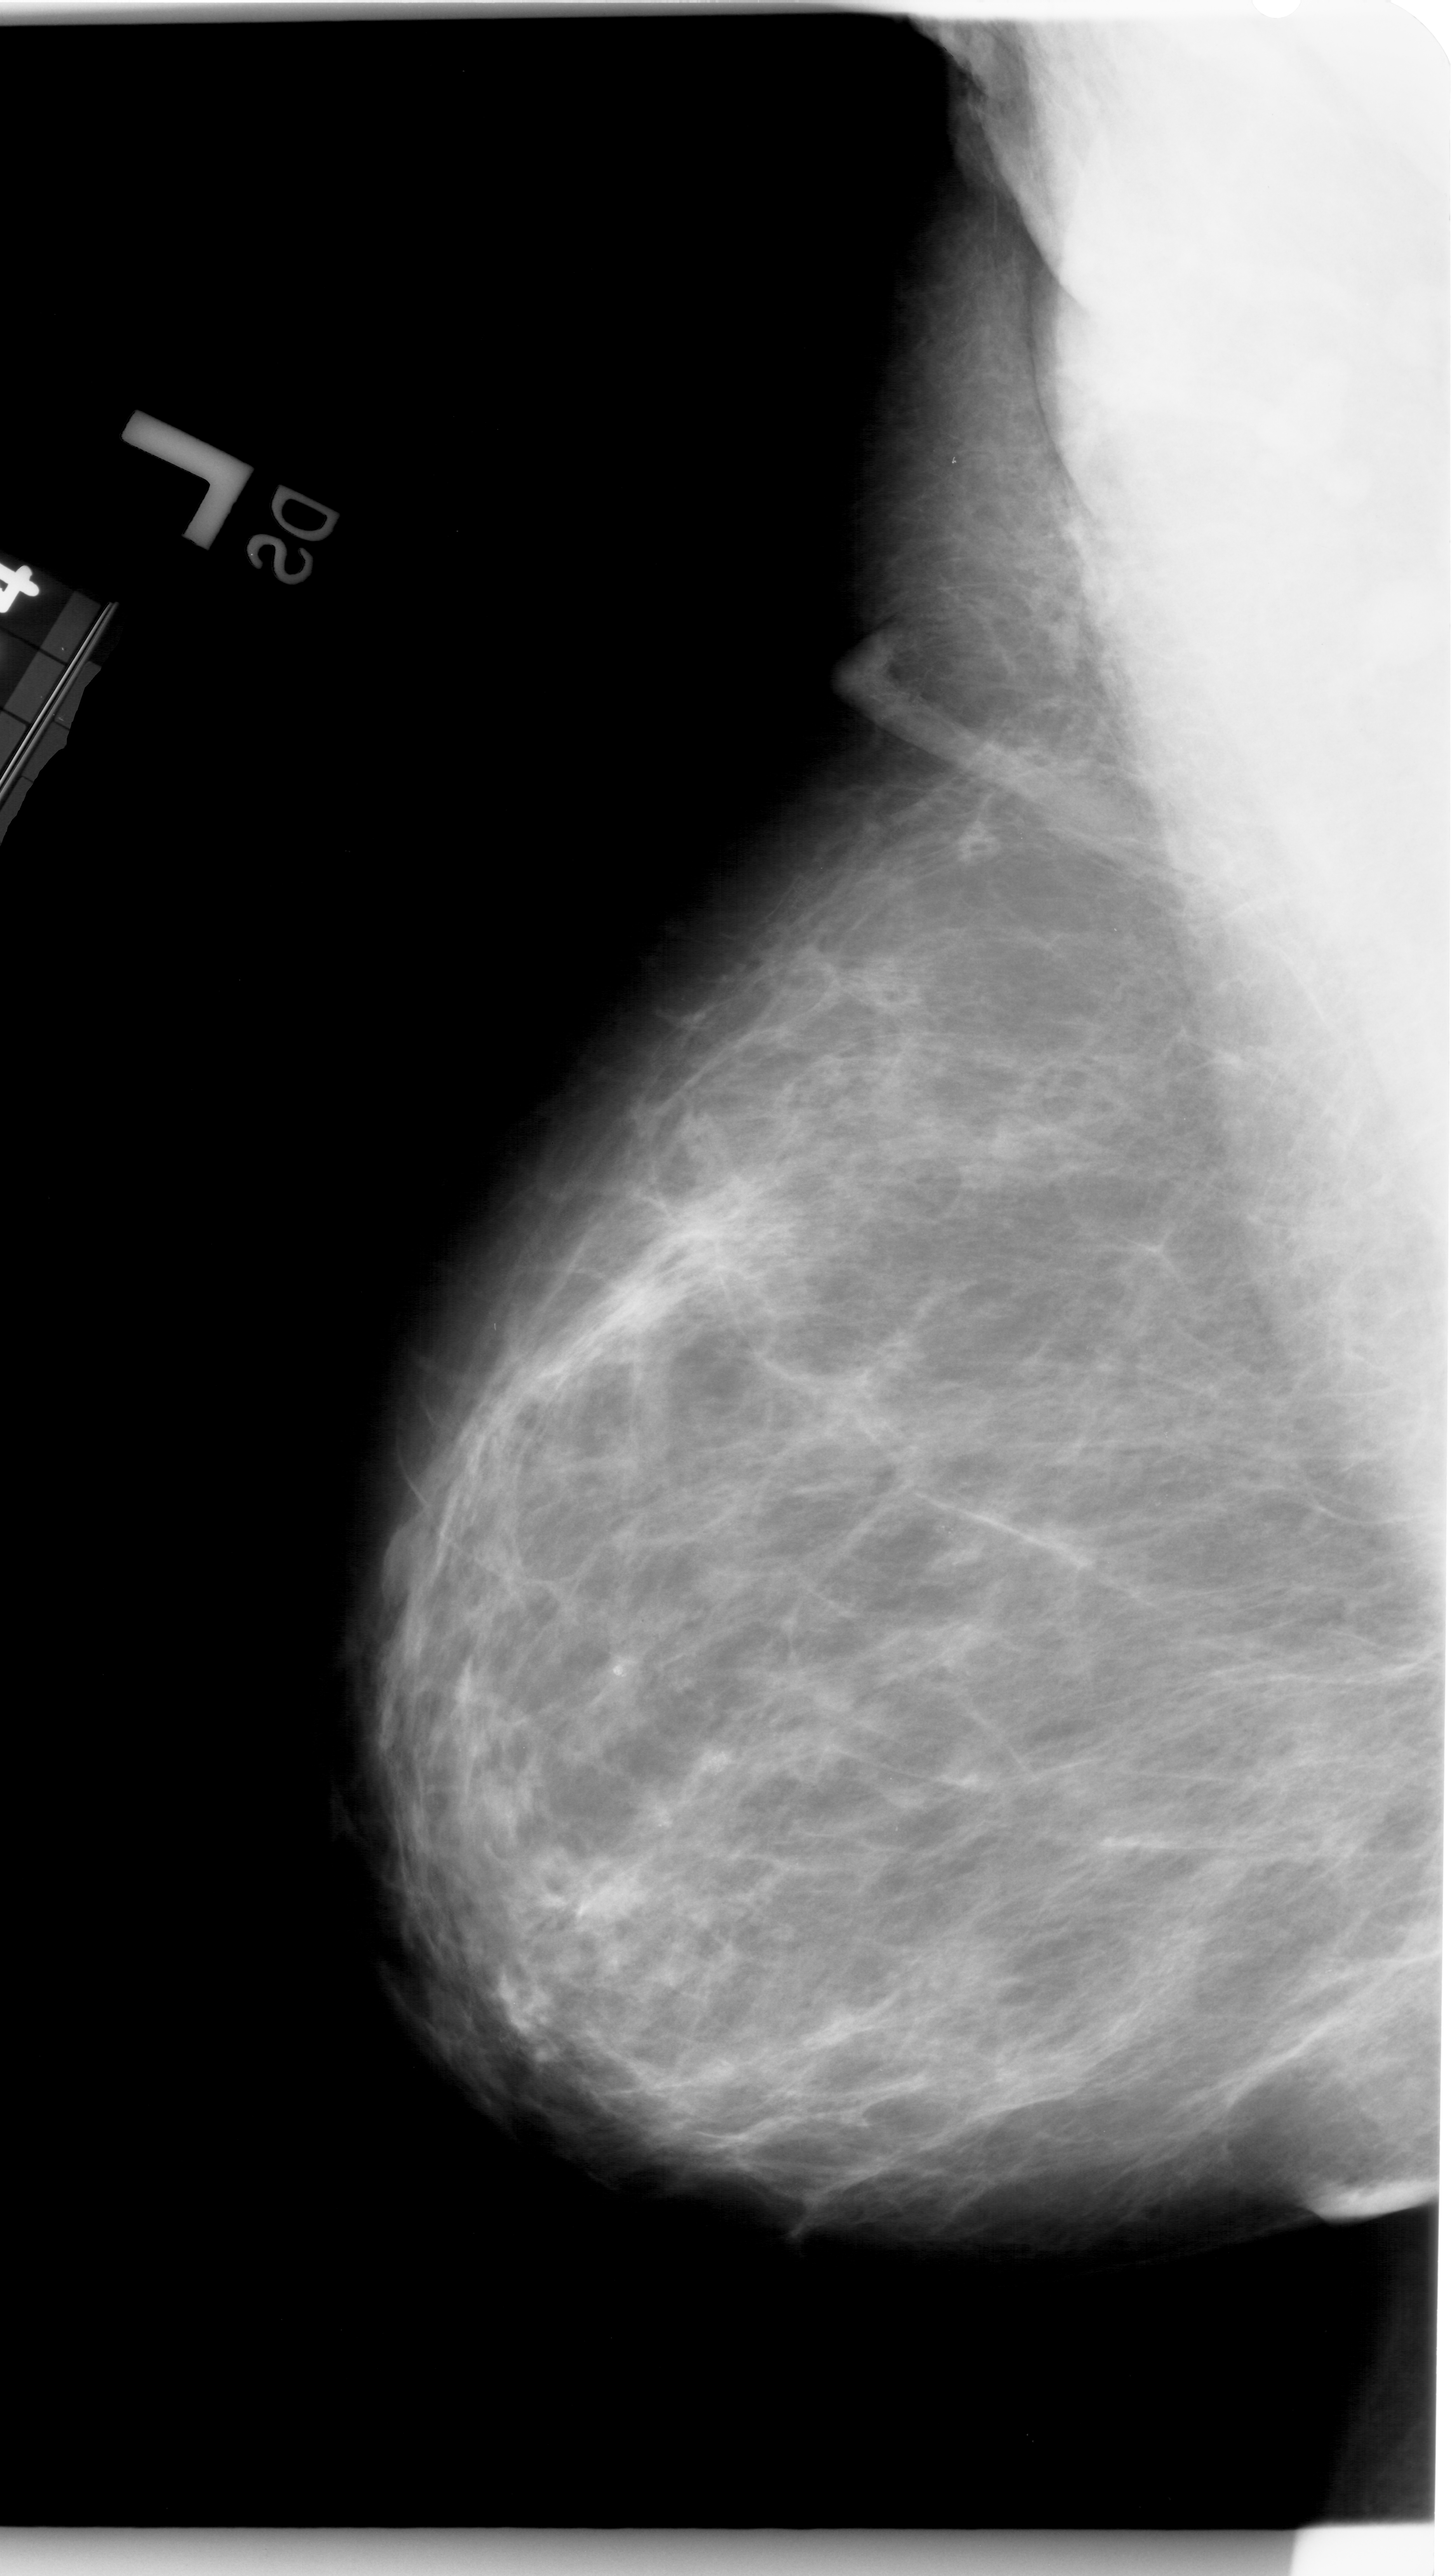
Mammogram (digitized film); left breast; MLO view; 1451 × 2576 image matrix.
Marked abnormalities (boxes around the expert regions of interest):
- calcifications, morphology pleomorphic, distribution clustered; BI-RADS assessment category 4; subtlety rating 2 on a 1 (subtle) to 5 (obvious) scale; pathology (as recorded): malignant: bounding box <637,1692,787,1839> (left, top, right, bottom; pixels)